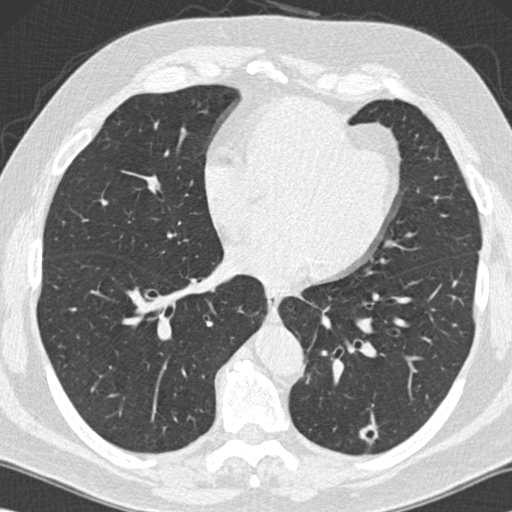
Low-dose screening chest CT, one axial slice. Slice 57 of 152 in the series (ordered by position). Reconstruction kernel B30f. 120 kVp. Lung window (W 1500 / L -600 HU). 2 mm slice thickness. 512 × 512 image matrix, field of view 350 × 350 mm.
Outlined on this slice (manually delineated by an expert):
- lesion 1 (tumor, lower lobe of left lung): bounding box <360,425,378,444> (left, top, right, bottom; pixels)